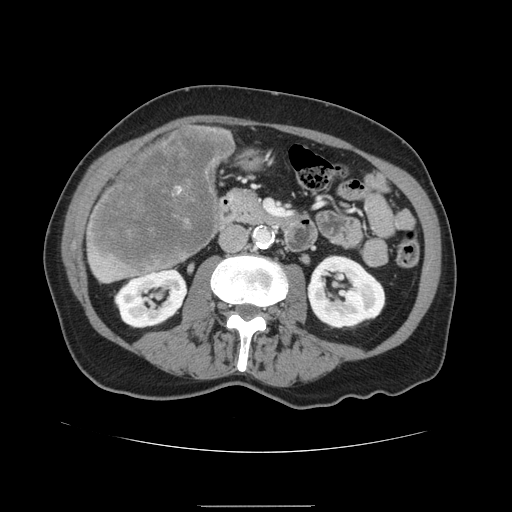
Contrast-enhanced abdominal CT, one axial slice; slice 44 of 168 in the series (ordered by position); 120 kVp; intravenous contrast given; soft-tissue window (W 400 / L 40 HU); 2.5 mm slice thickness; 512 × 512 image matrix, field of view 386 × 386 mm. Male patient, age 74 years. From the clinical record (not read from this slice): diagnosis: colorectal cancer liver metastases, imaged before liver resection; multiple liver metastases: no; largest metastasis: 14.5 cm; disease in both lobes: yes.
Structures marked on this image (manually delineated by an expert):
- liver: box from (x=85, y=125) to (x=235, y=284) px
- liver metastasis: (x=90, y=129)–(x=232, y=270)